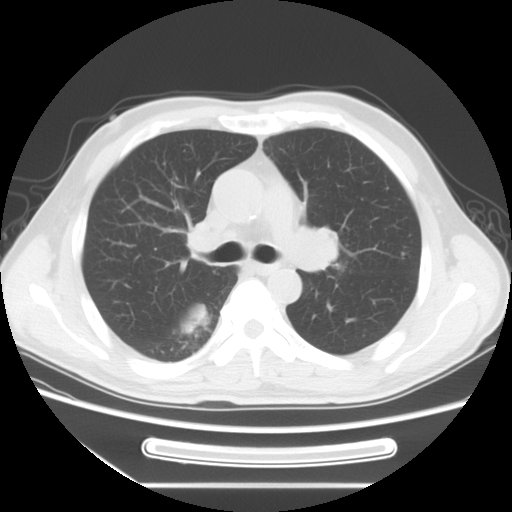
Chest CT, one axial slice; slice 46 of 71 in the series (ordered by position); reconstruction kernel STANDARD; 120 kVp; lung window (W 1500 / L -600 HU); 512 × 512 image matrix, field of view 366 × 366 mm. Patient: male, 51 years. Case-level facts recorded for this patient, not image findings: clinical TNM (as recorded): T1c N3 M0.
Annotated regions visible in this slice (rectangle marked by the reading radiologist):
- lung tumour (recorded histology: adenocarcinoma): box from (x=289, y=212) to (x=354, y=287) px